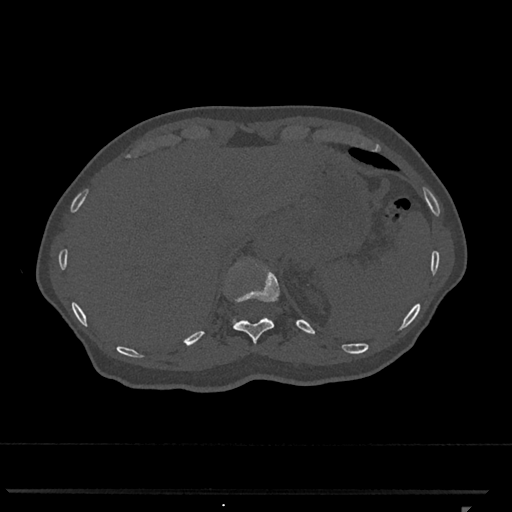
CT including the spine, one axial slice. Position 507 of 793 along the scan axis. Reconstruction kernel Br40s/3. Bone window (W 1800 / L 400 HU). 0.5 mm slice thickness. 512 × 512 image matrix, field of view 380 × 380 mm. Female patient, age 62 years. Case-level facts recorded for this patient, not image findings: primary cancer: renal.
Annotated regions visible in this slice (semi-automatically segmented with operator editing):
- T11 vertebra: box from (x=233, y=260) to (x=280, y=344) px
- T12 vertebra: (x=233, y=319)–(x=236, y=322)